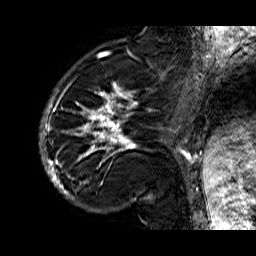
Breast MRI (dynamic contrast-enhanced), one sagittal slice. Position 15 of 60 along the scan axis. Dynamic contrast-enhanced series, time point 2 of 6 at this slice position (early post-contrast). 1.5 T. TE 6.3 ms, TR 32.9 ms. 4 mm slice thickness. 256 × 256 image matrix. Female patient. Case-level facts recorded for this patient, not image findings: setting: breast cancer imaged before/during neoadjuvant chemotherapy; receptor status: HR-positive, HER2-negative.
Annotated regions visible in this slice (semi-automatic segmentation, software-assisted and operator-edited):
- analysis volume of interest (the breast-tissue region the enhancement analysis was run in; not a lesion): bounding box [x1, y1, x2, y2] px = [39, 74, 176, 210]
- tumour enhancement mask (voxels above the 100 % enhancement threshold inside the analysis volume of interest): [39, 74, 176, 200]